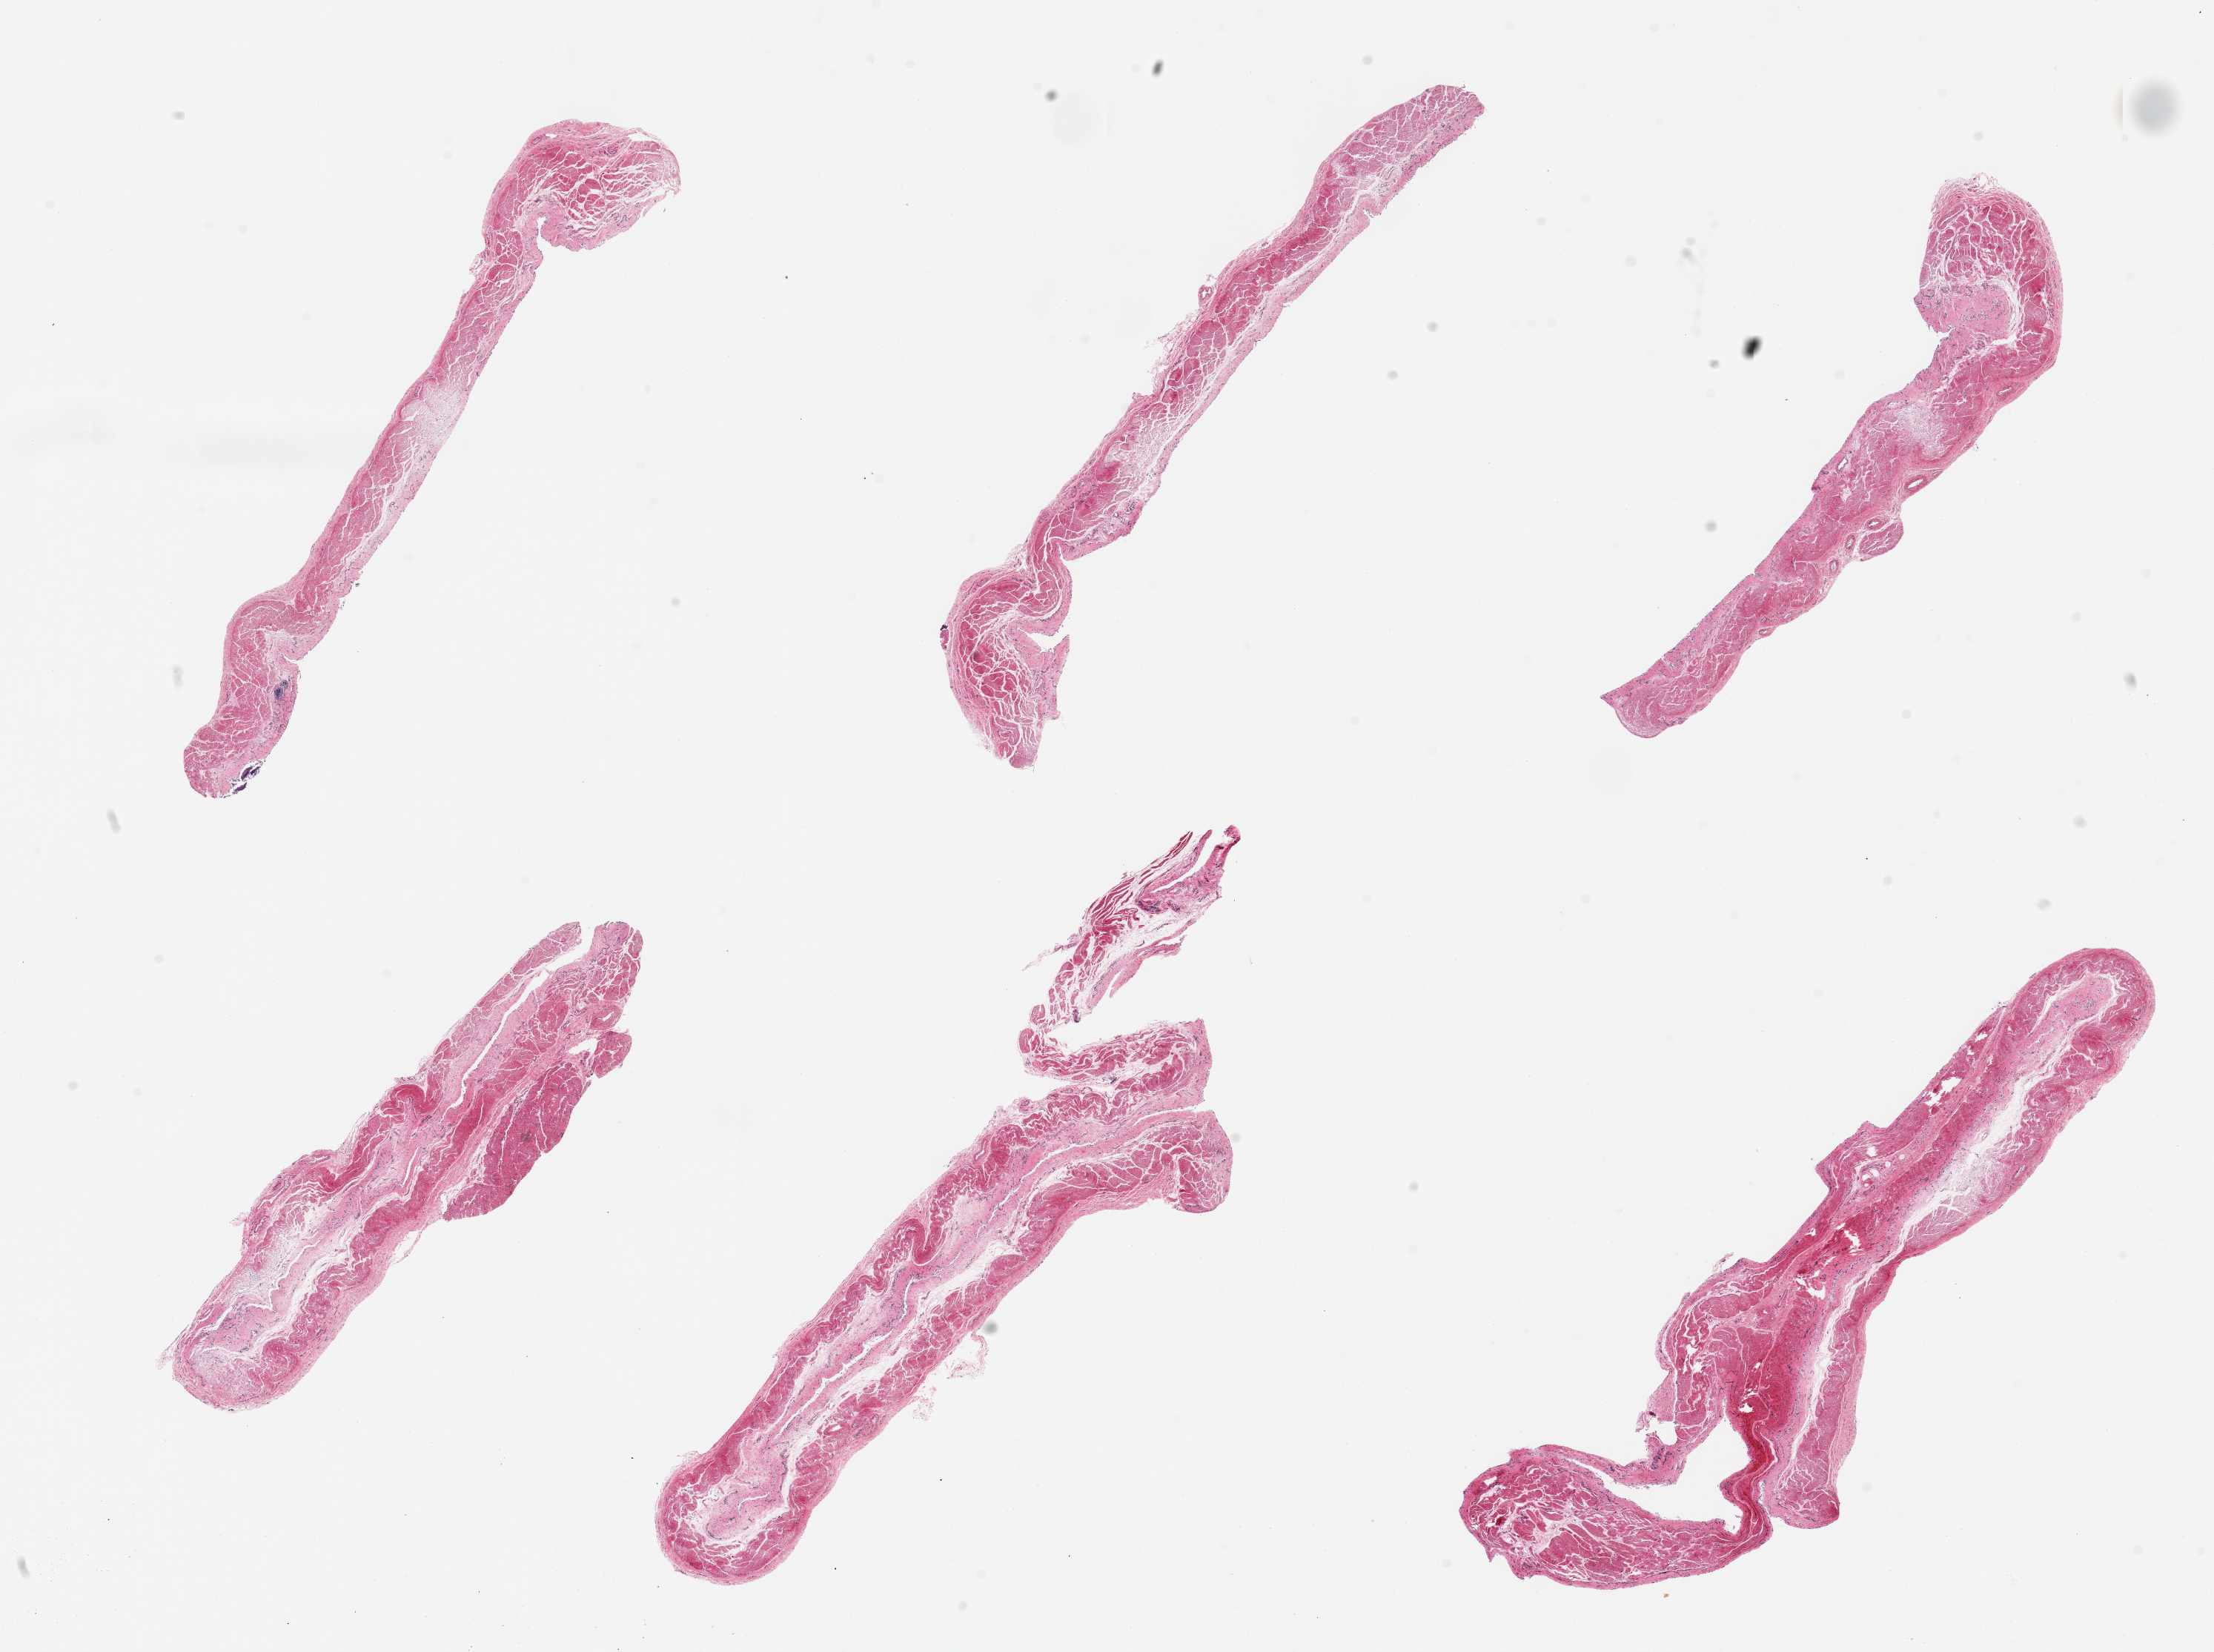
Haematoxylin and eosin whole-slide image — whole scanned area (about 23.6 x 17.6 mm, acquisition: 20x scan) shown as a low-resolution overview. PAXgene-fixed paraffin-embedded (PFPE) section. Section of esophageal mucous membrane (target tissue). Donor tissue sample. Donor: male.
- reviewer comment on this tissue sample: 6 pieces, mucosa completely sloughed save for minute fragment, unusually poorly preserved